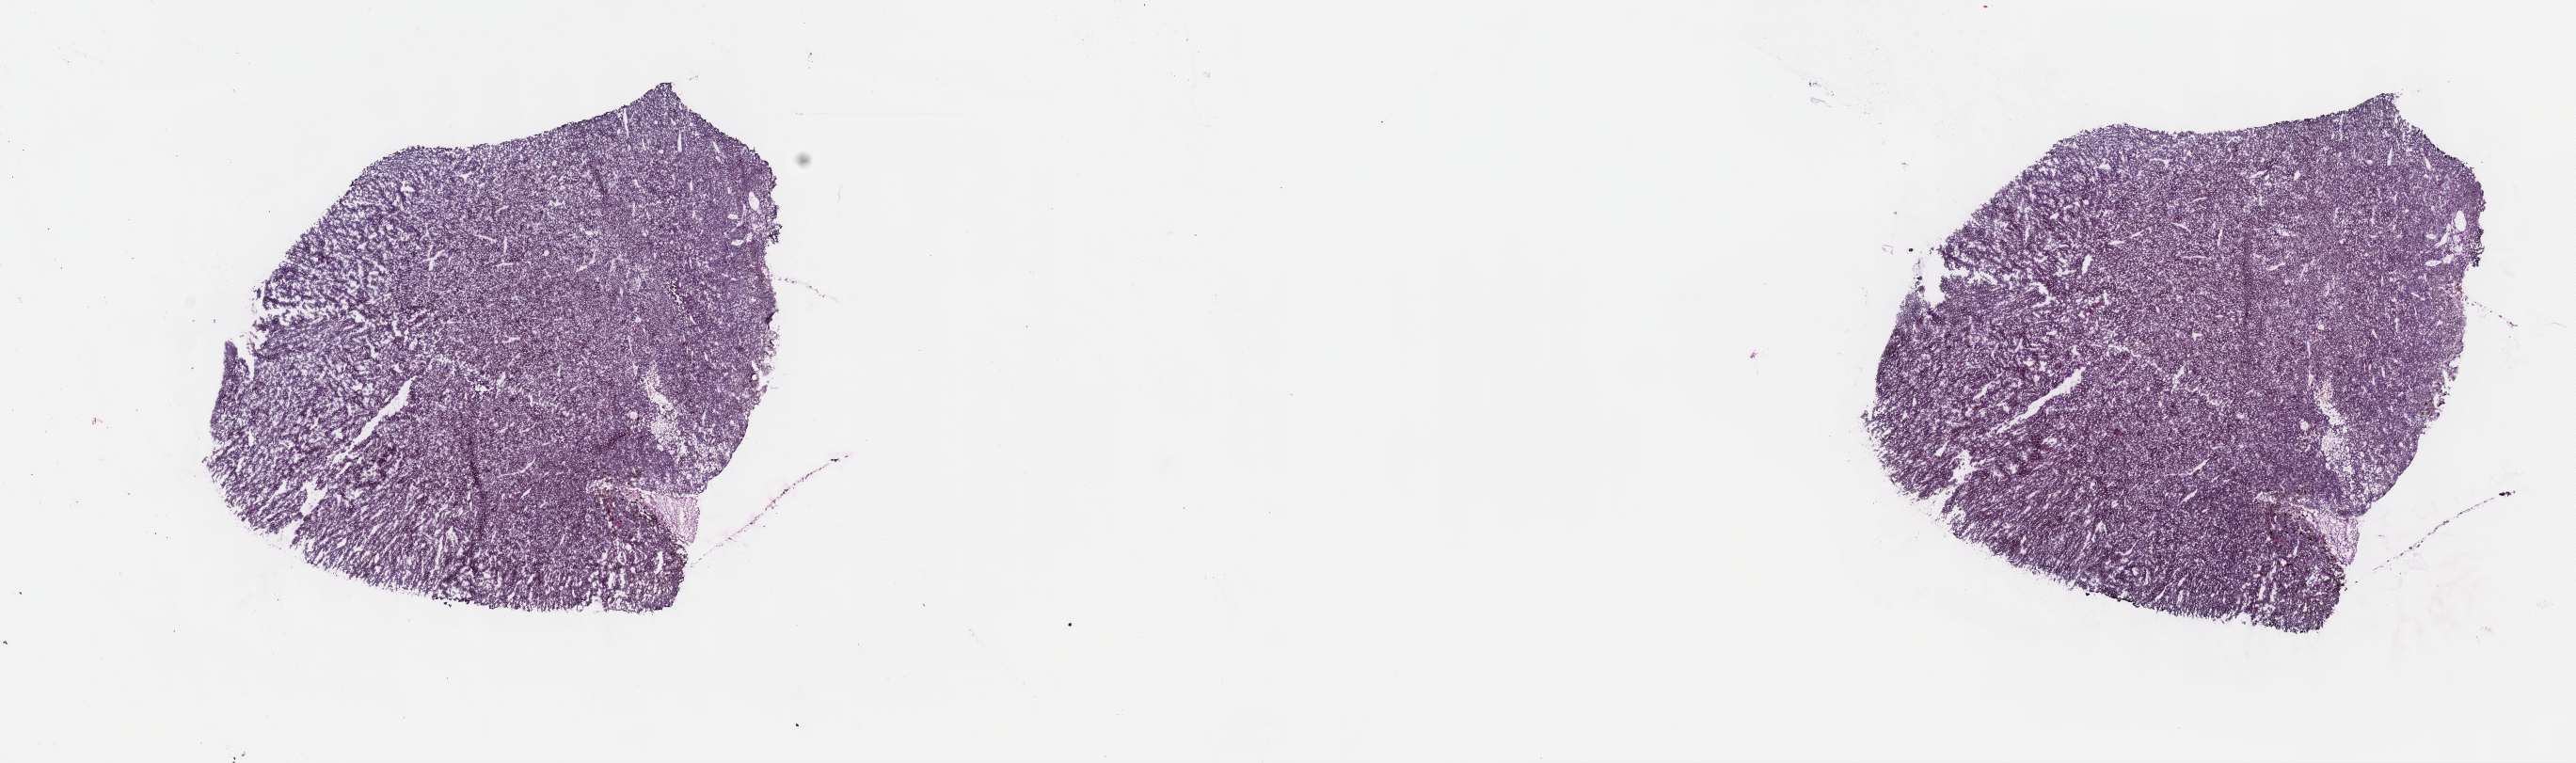
Whole-slide histology image, Hematoxylin and eosin (H&E) stained, whole scanned area (about 22.1 x 6.6 mm, slide scanned at 40x) shown as a low-resolution overview, frozen section from the top of the tissue portion, primary tumour sample from the uvea. Patient: male, age at initial diagnosis 54 years. Pathologist review of this section (percent, as recorded): tumour cells 100%, tumour nuclei 80%, normal cells 0%, stromal cells 0%, necrosis 0%. Inflammatory infiltration, as recorded: lymphocyte infiltration 1%, monocyte infiltration 0%, neutrophil infiltration 0%.
Pathologic diagnosis: Spindle cell melanoma, type B (choroid). TNM: T4a NX MX. Laterality: left. AJCC pathologic stage: IIIA (7th edition).